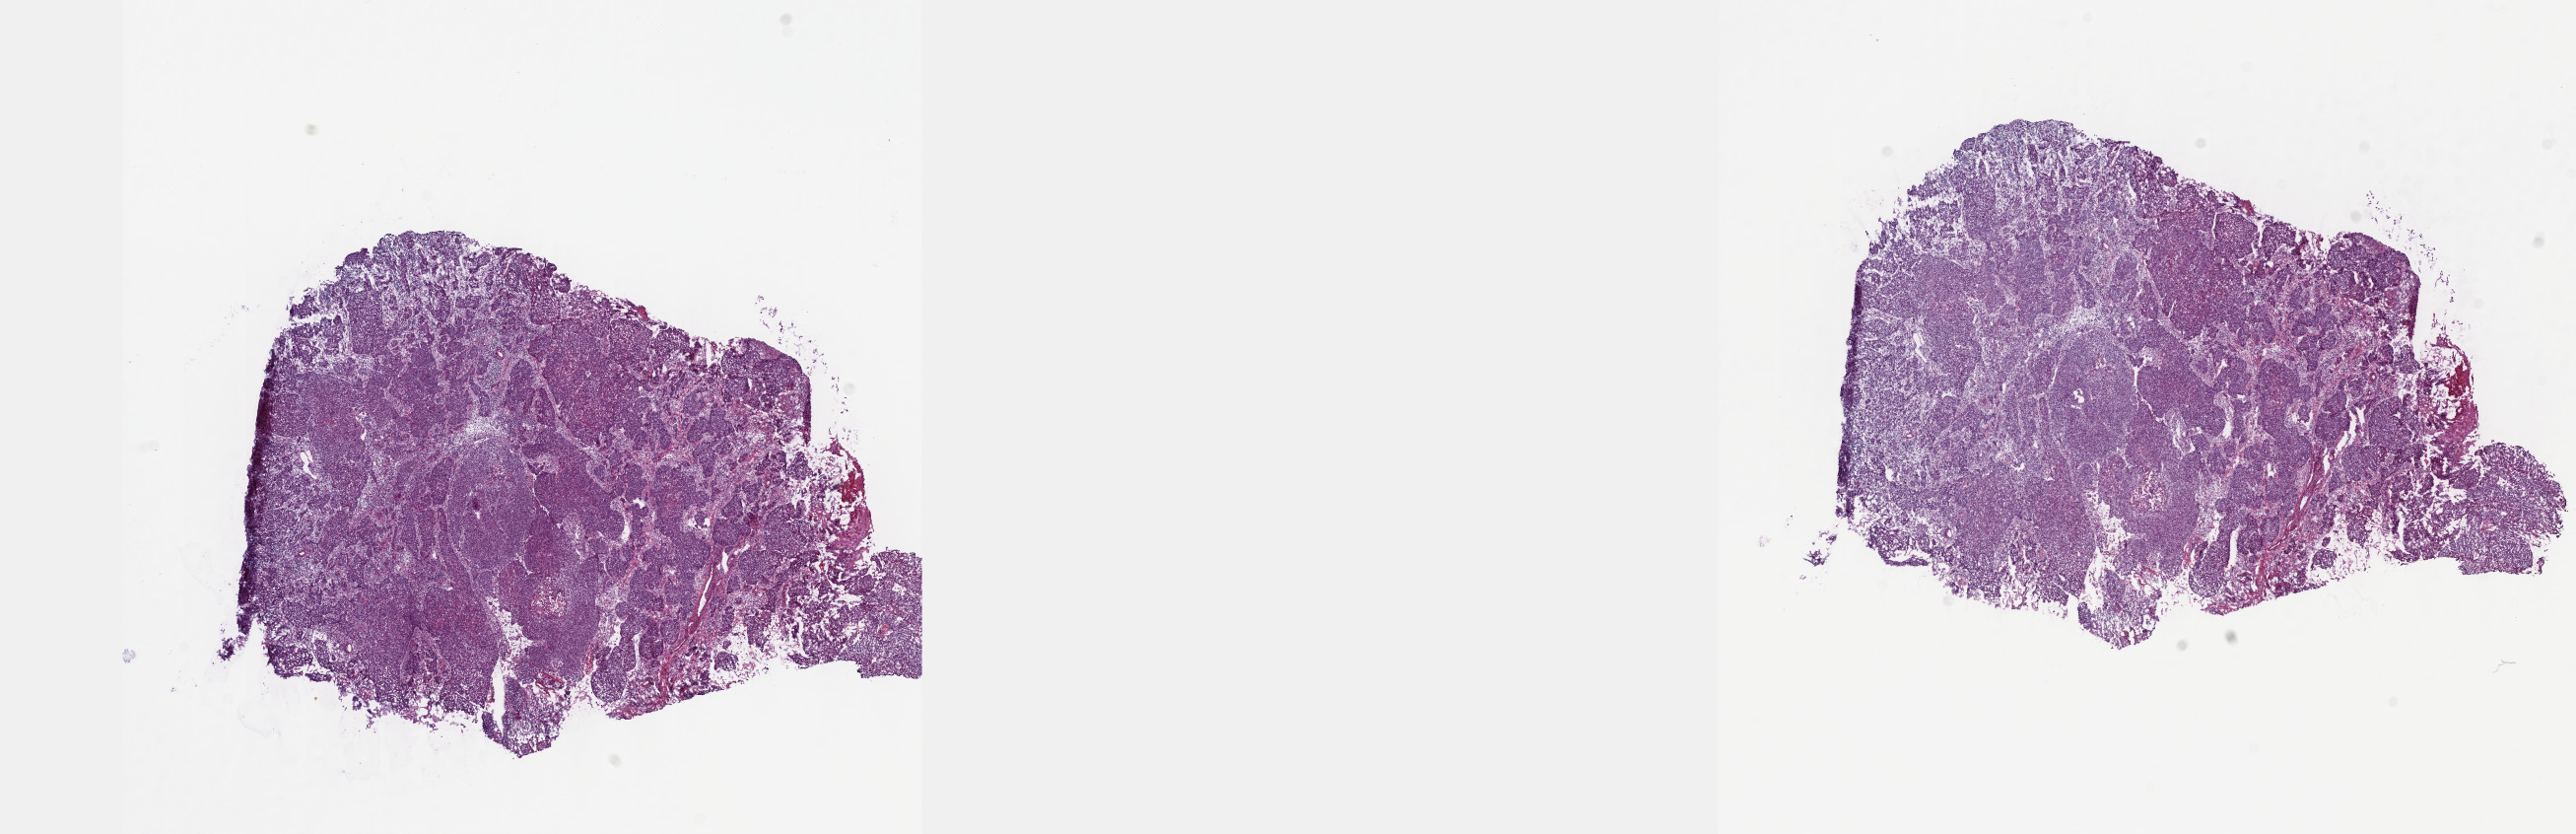
Whole-slide histology image, H&E-stained, shown as a low-resolution overview of the whole scanned area (about 21.1 x 6.8 mm), frozen section, cervix, primary tumour sample. Female, age 39 years at initial diagnosis. Slide review estimates, as recorded: tumour cells 75%, tumour nuclei 75%.
Histologic diagnosis: Squamous cell carcinoma, NOS (cervix uteri).